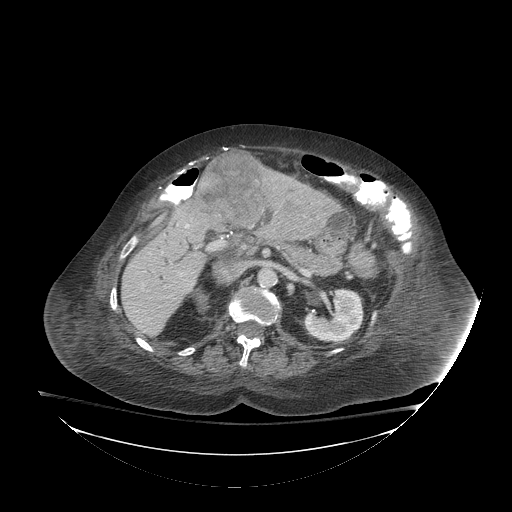
Contrast-enhanced abdominal CT (liver protocol), one axial slice; position 41 of 81 along the scan axis; reconstruction kernel STANDARD; 140 kVp; soft-tissue window (W 400 / L 40 HU); 512 × 512 image matrix, field of view 500 × 500 mm. Case-level facts recorded for this patient, not image findings: diagnosis: hepatocellular carcinoma (patient treated with transarterial chemoembolisation; whether this scan precedes or follows treatment is not stated here); TNM stage (as recorded): Stage-I.
Outlined on this slice (semi-automatic segmentation, software-assisted and operator-edited):
- liver parenchyma outside the tumour (the mass and vessels are separate outlines, so this box may not span the whole liver): bounding box [x1, y1, x2, y2] px = [121, 169, 338, 336]
- mass: [198, 151, 268, 227]
- liver vessels: [185, 224, 190, 228]